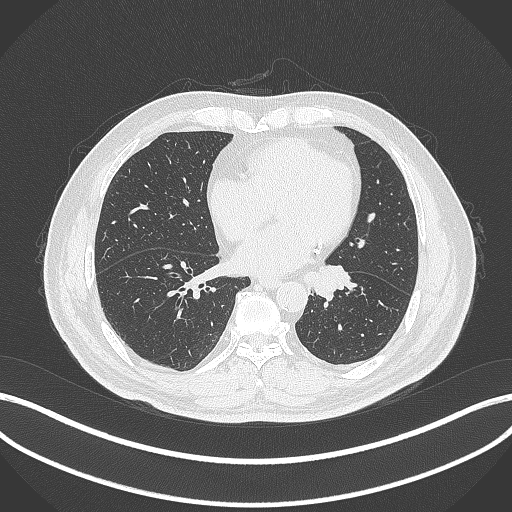
Chest CT, one axial slice; slice 107 of 312 in the series (ordered by position); reconstruction kernel B70f; lung window (W 1500 / L -600 HU); 1 mm slice thickness; 512 × 512 image matrix, field of view 400 × 400 mm. Patient: male, 71 years. From the clinical record (not read from this slice): clinical TNM (as recorded): T1b N0 M0.
Annotated regions visible in this slice (bounding box drawn by a radiologist):
- lung tumour (recorded histology: squamous cell carcinoma): box from (x=302, y=261) to (x=358, y=303) px